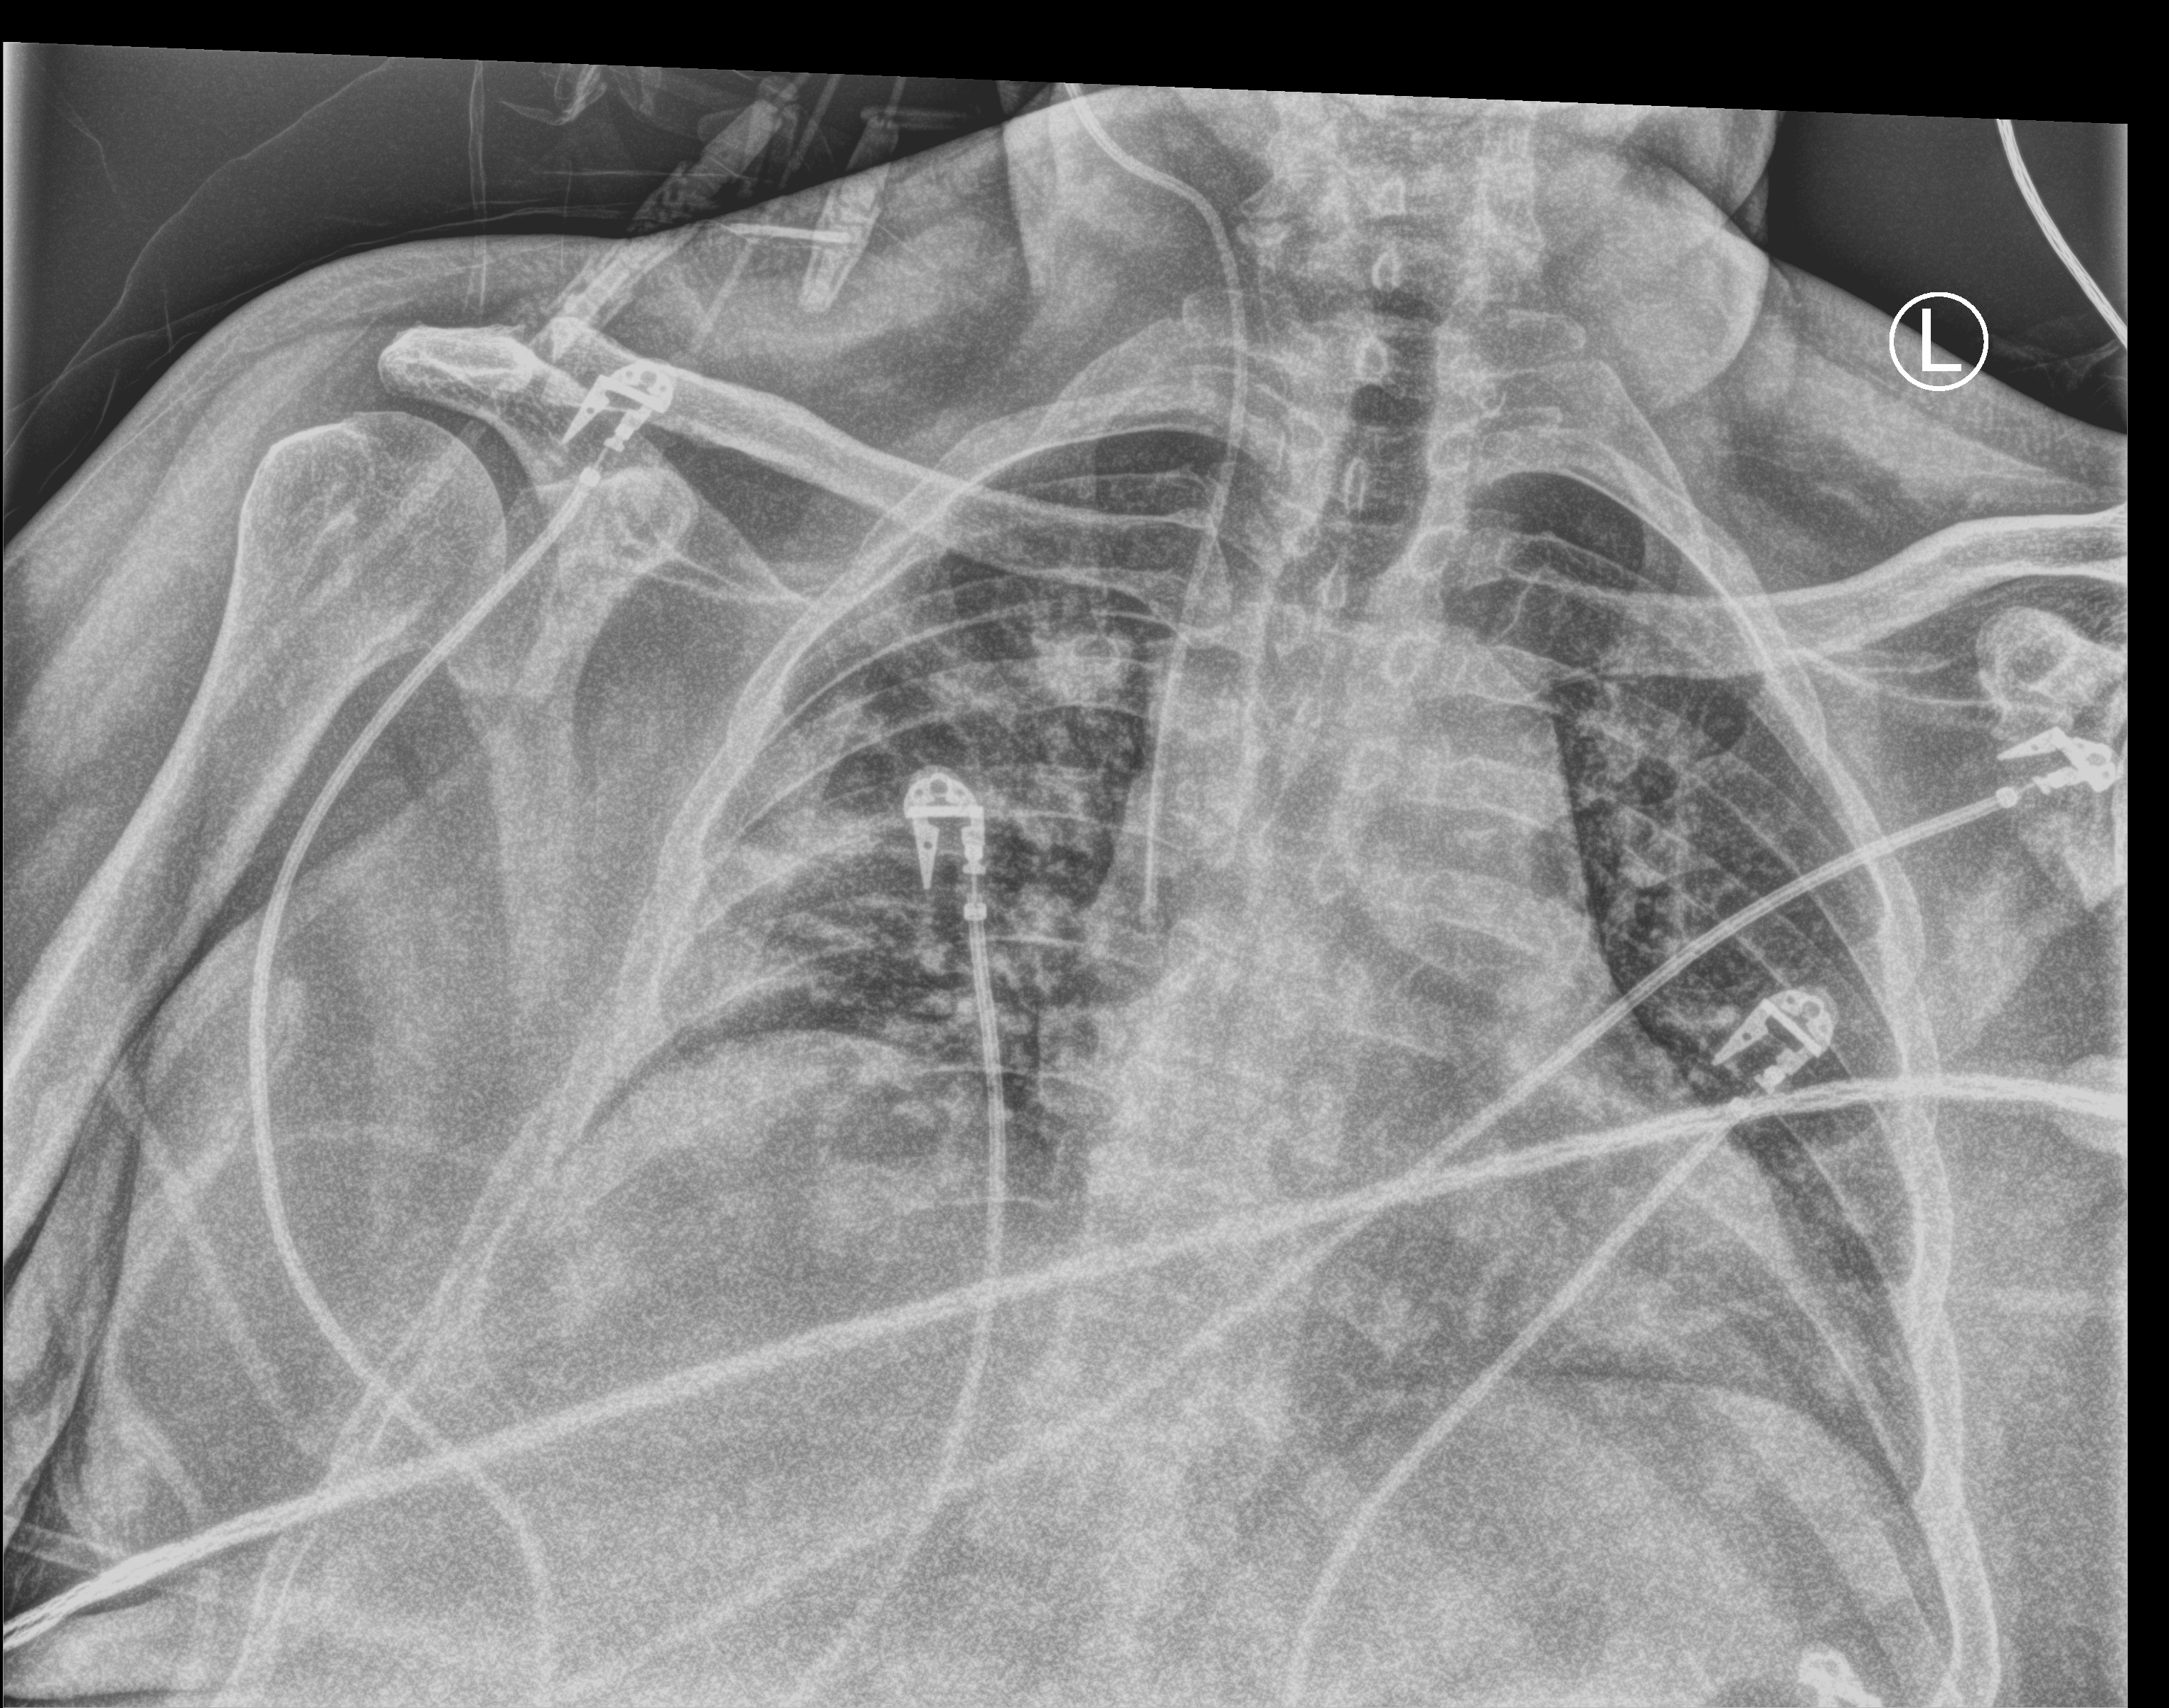
Portable chest radiograph; anteroposterior (AP) projection. Patient hospitalised with COVID-19; male, aged 60–74 years.
From the hospital-stay record, not from the radiograph (when in the stay this image was taken is not recorded):
- admitted to intensive care during this hospital stay: yes
- mechanically ventilated during this hospital stay: no